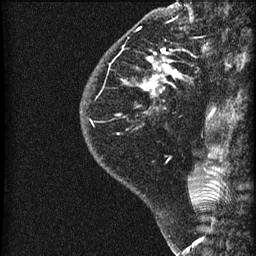
Breast MRI (dynamic contrast-enhanced), one sagittal slice; position 18 of 60 along the scan axis; dynamic contrast-enhanced series, image 2 of 3 at this slice position (ordered by acquisition); 1.5 T; TE 4.2 ms, TR 22.7 ms; 1.8 mm slice thickness; 256 × 256 image matrix, field of view 180 × 180 mm. Female patient, age 45 years. Case-level facts recorded for this patient, not image findings: setting: breast cancer imaged before/during neoadjuvant chemotherapy; receptor status: HR-positive, HER2-negative.
Annotated regions visible in this slice (semi-automatically segmented with operator editing):
- analysis volume of interest (the breast-tissue region the enhancement analysis was run in; not a lesion): bounding box (x1, y1, x2, y2) in pixels: (81, 11, 205, 140)
- tumour enhancement mask (voxels above the 90 % enhancement threshold inside the analysis volume of interest): (143, 48, 176, 94)